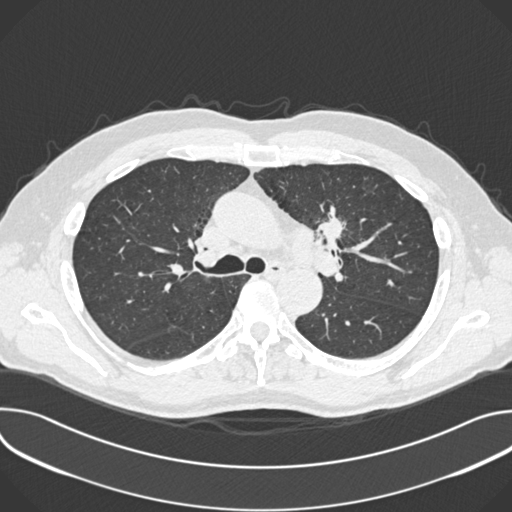
Low-dose screening chest CT, one axial slice; position 250 of 361 along the scan axis; reconstruction kernel B30f; 120 kVp; lung window (W 1500 / L -600 HU); 1 mm slice thickness; 512 × 512 image matrix, field of view 380 × 380 mm.
Structures marked on this image (outlined manually by an expert reader):
- lesion 1 (tumor, upper lobe of left lung): bounding box <315,209,345,248> (left, top, right, bottom; pixels)